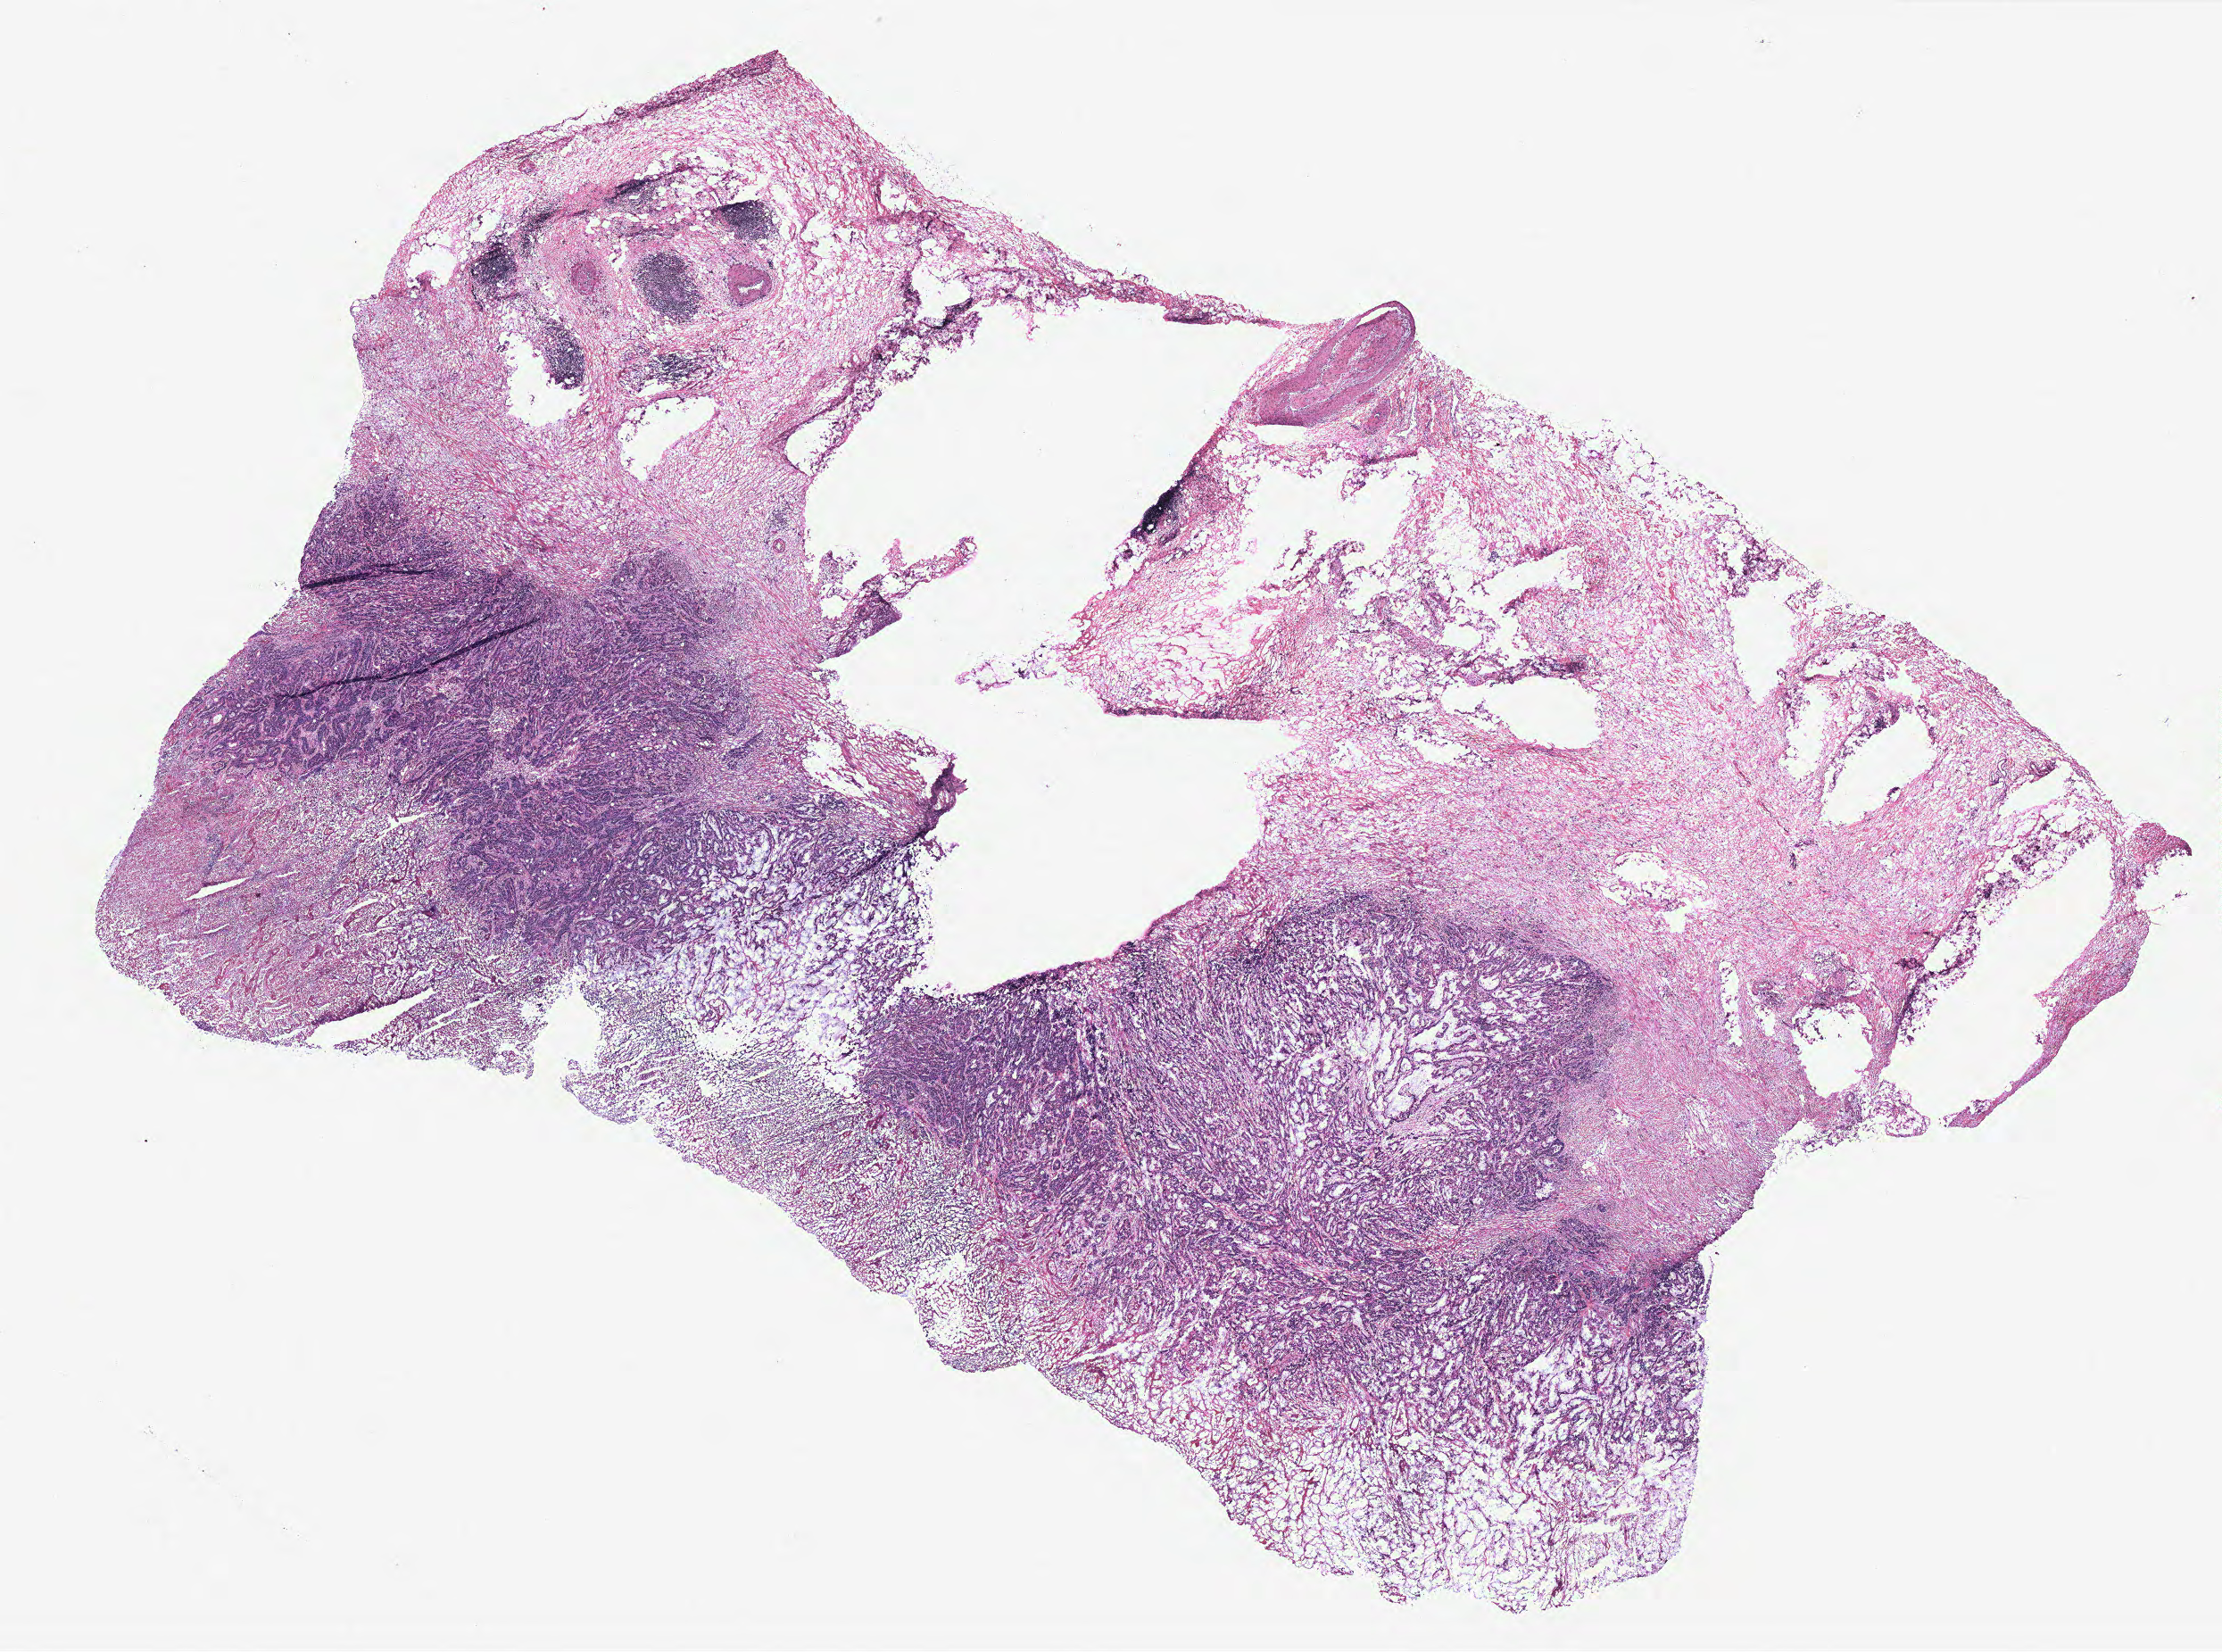
Whole-slide histology image, H&E-stained — a low-resolution overview of the entire scanned area, about 19.9 x 14.8 mm (slide scanned at 40x). Colon, tissue type not recorded. Patient sex: female.
Patient diagnosis: Adenocarcinoma, NOS.